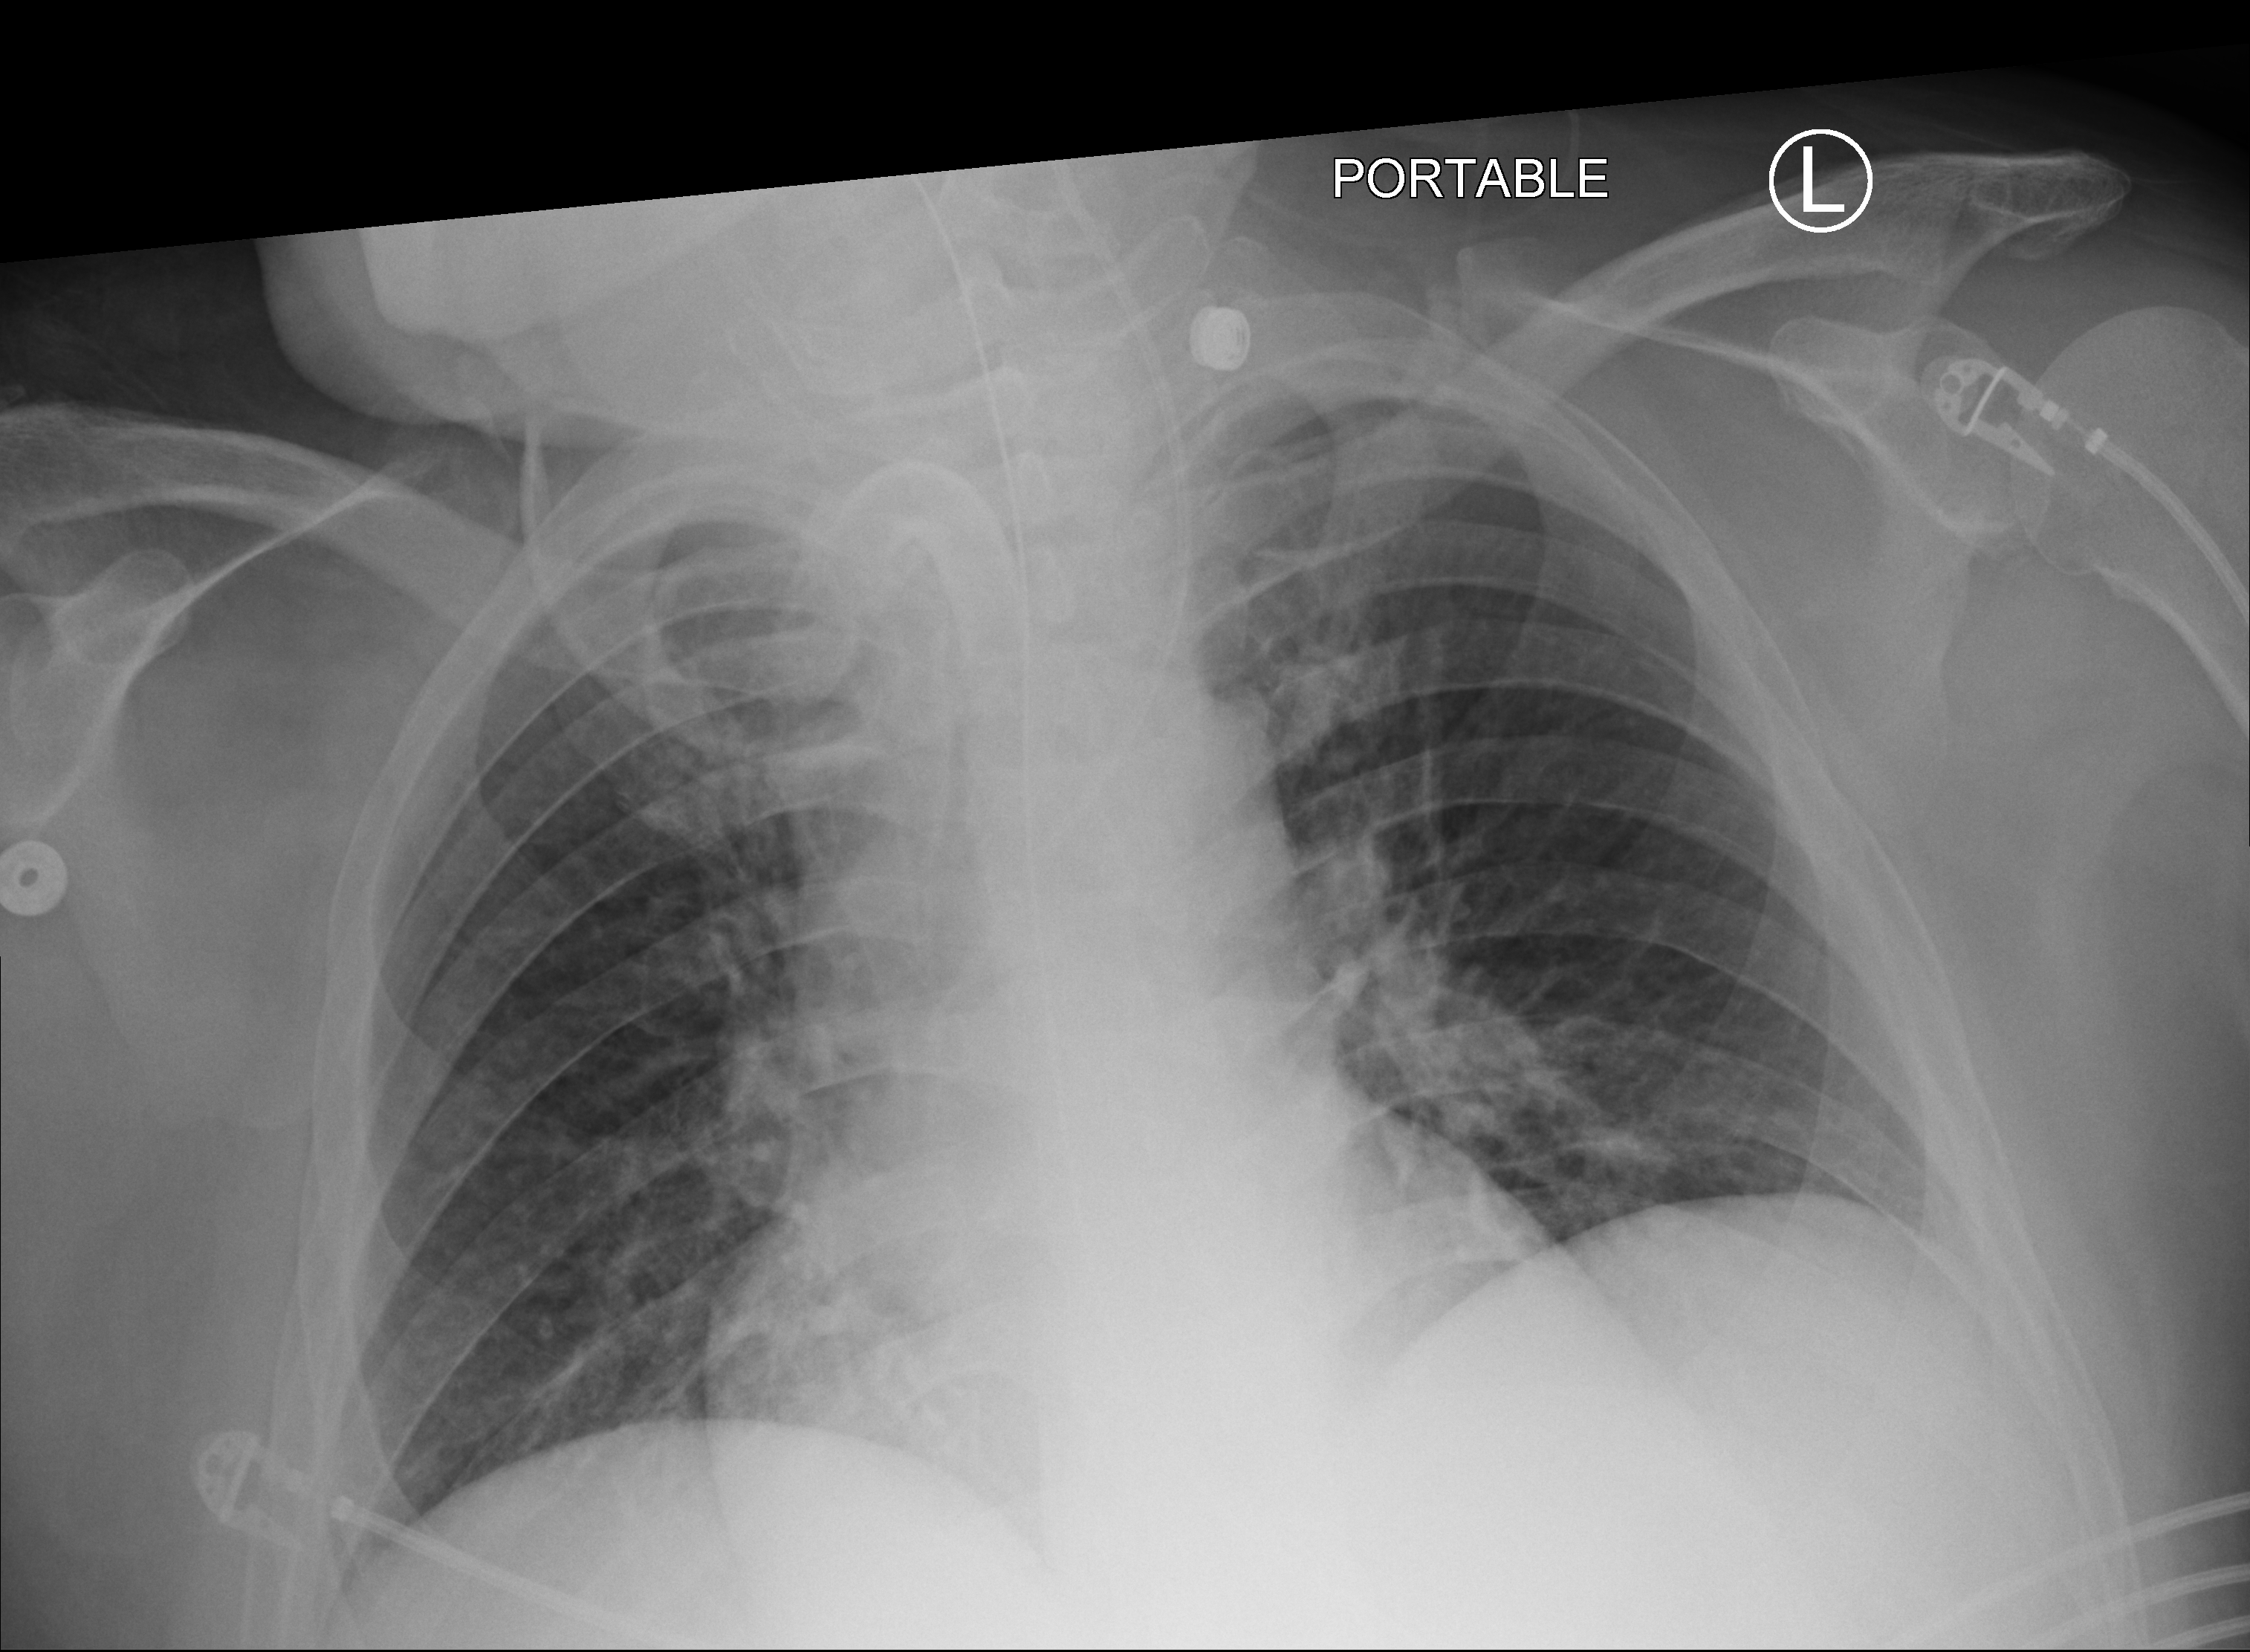
Chest X-ray (portable), anteroposterior (AP) projection. Patient hospitalised with COVID-19; male, aged 18–59 years.
Admission-level facts for this patient (not findings on this image; timing relative to this image not recorded):
- length of hospital stay: 65 days
- admitted to intensive care during this hospital stay: yes